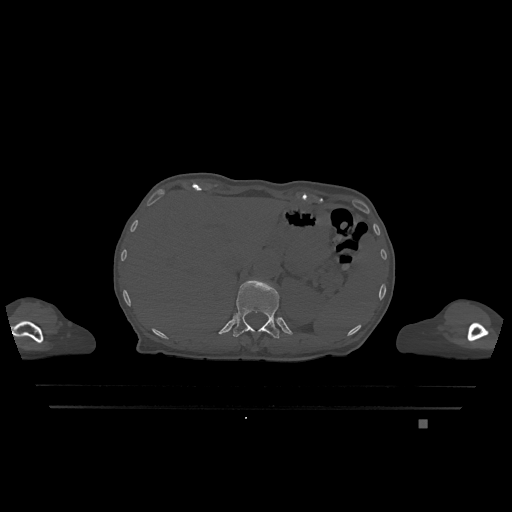
CT including the spine, one axial slice; slice 535 of 1317 in the series (ordered by position); bone window (W 1800 / L 400 HU); 0.5 mm slice thickness; 512 × 512 image matrix, field of view 500 × 500 mm. Patient: female, 74 years. From the clinical record (not read from this slice): primary cancer: lung; vertebrae with lytic lesions (as recorded): T1, T4, T5, T6, L4, L5.
Outlined on this slice (semi-automatically segmented with operator editing):
- T12 vertebra: box from (x=233, y=280) to (x=279, y=338) px